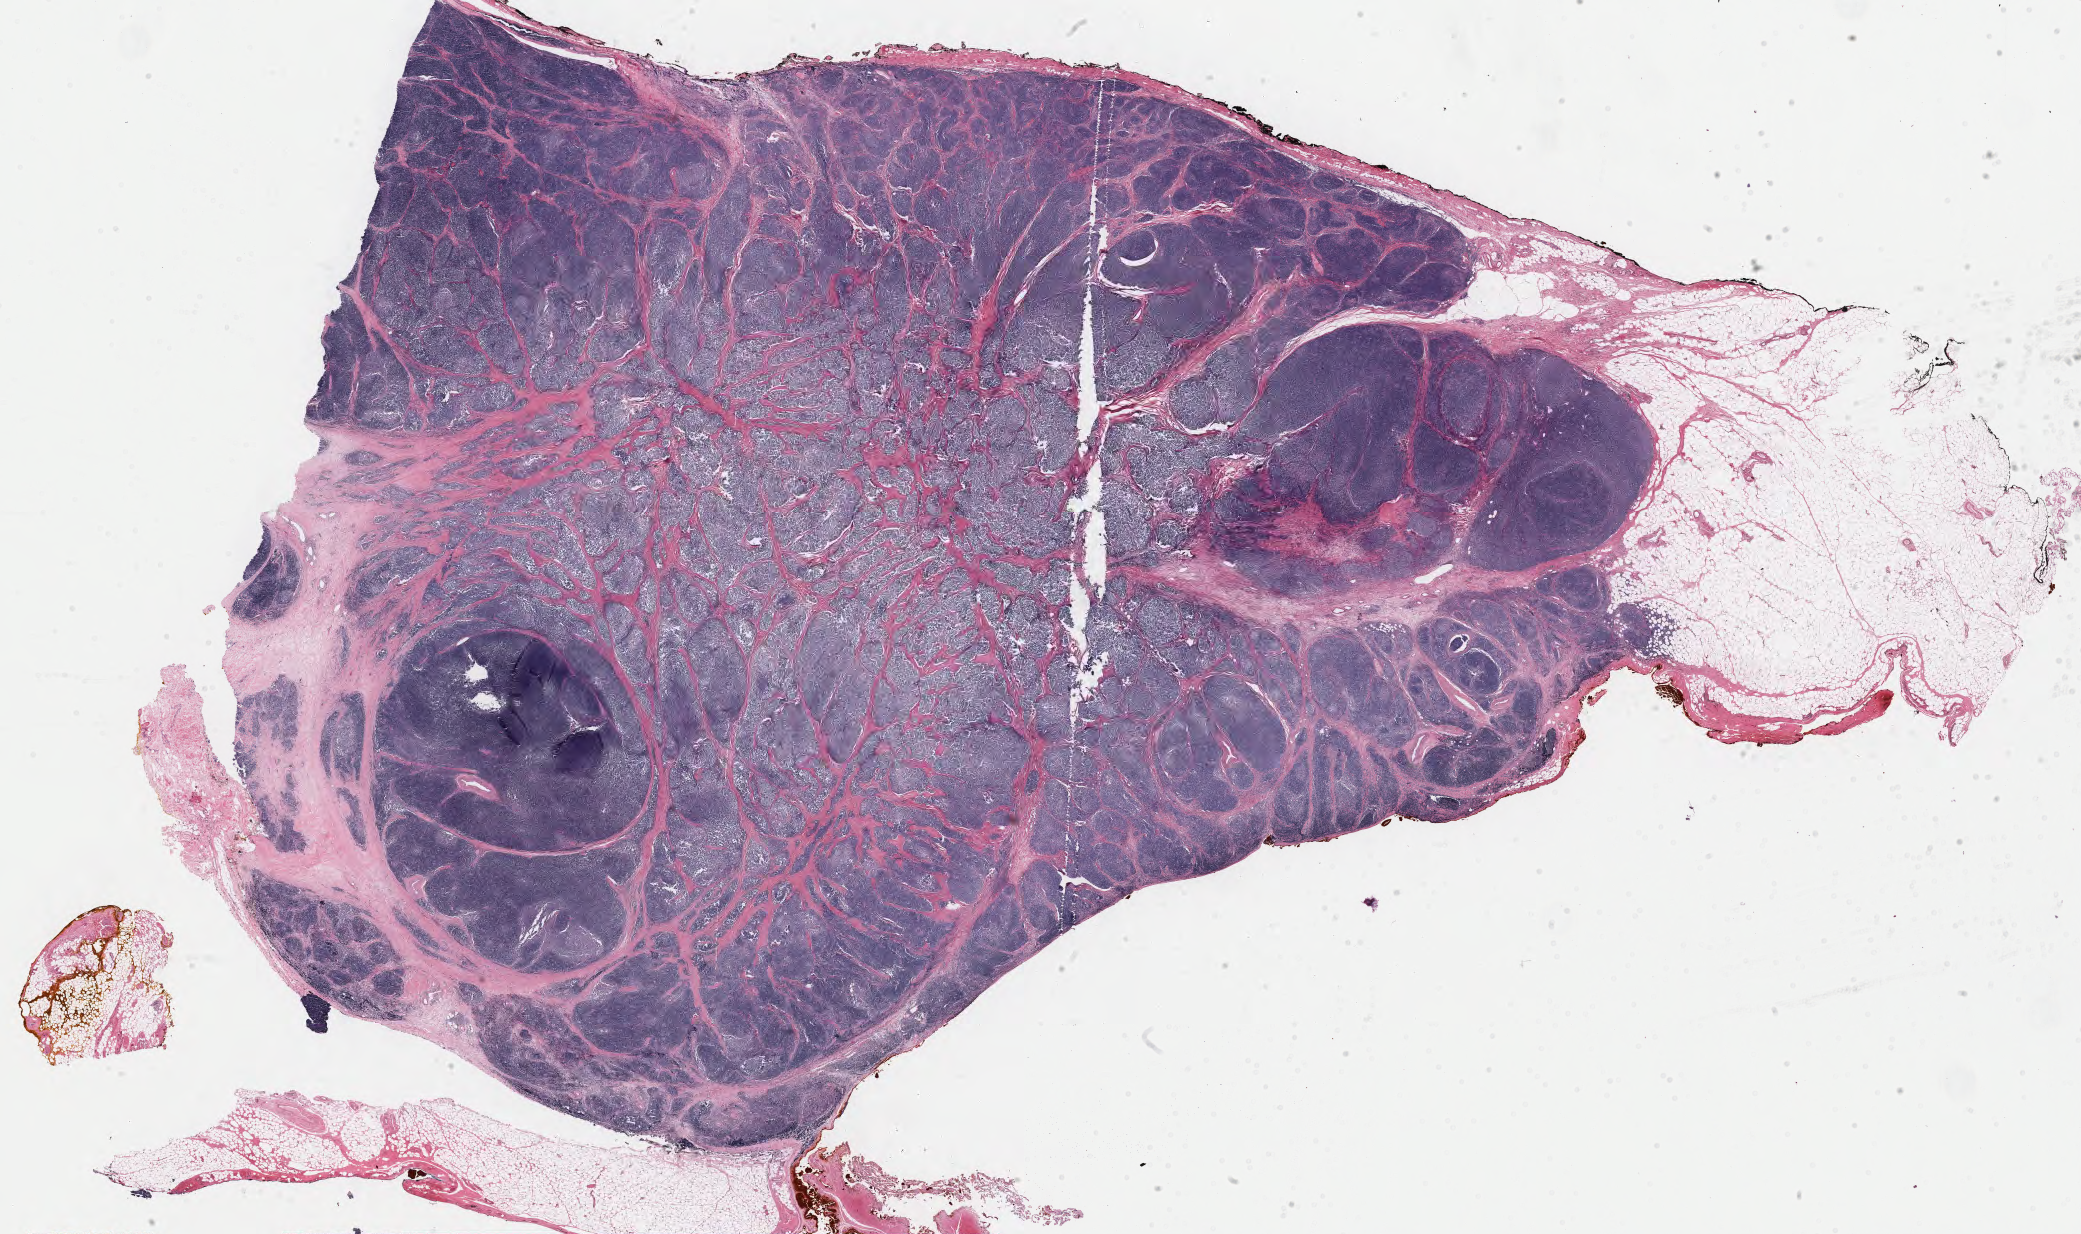
Whole-slide histology image, H&E-stained, shown as a low-resolution overview of the whole scanned area (about 33.0 x 19.6 mm, slide scanned at 40x), formalin-fixed paraffin-embedded (FFPE) diagnostic section, sample: primary tumour, thymus. Patient: female, age at initial diagnosis 57 years.
Histologic diagnosis: Thymoma, type B1, NOS.